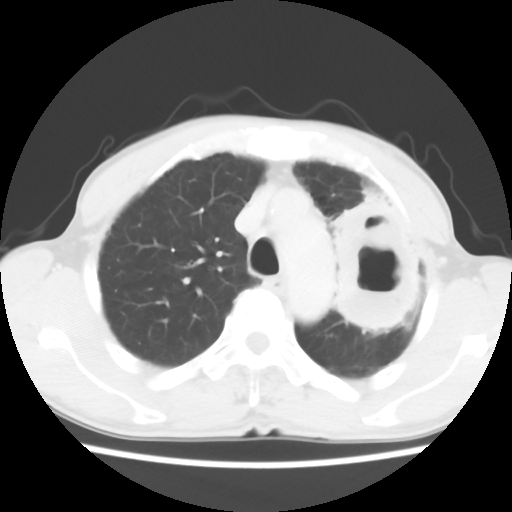
Chest CT, one axial slice; position 45 of 60 along the scan axis; reconstruction kernel STANDARD; lung window (W 1500 / L -600 HU); 512 × 512 image matrix. Patient: male, 64 years. From the clinical record (not read from this slice): clinical TNM (as recorded): T3 N3 M0; histopathological grade: G3.
Annotated regions visible in this slice (bounding box drawn by a radiologist):
- lung tumour (recorded histology: adenocarcinoma): bounding box <324,183,434,348> (left, top, right, bottom; pixels)